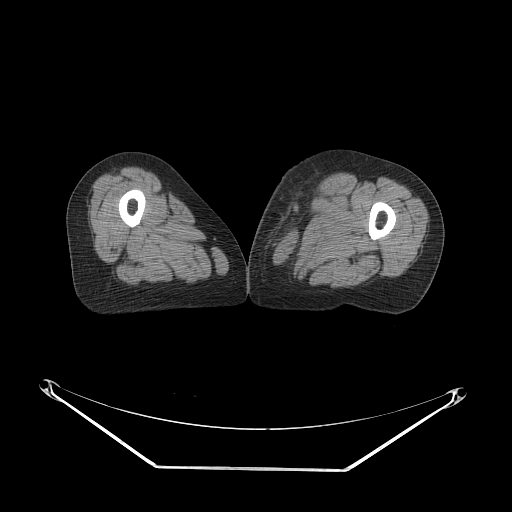
CT of an extremity soft-tissue mass (from a PET/CT study), one axial slice. Position 49 of 91 along the scan axis. Soft-tissue window (W 400 / L 40 HU). 512 × 512 image matrix, field of view 500 × 500 mm. Female patient. From the clinical record (not read from this slice): histological type: pleomorphic leiomyosarcoma; grade: high; site of the primary tumour: left thigh.
Outlined on this slice (expert contour drawn on MRI and transferred to this co-registered scan by the dataset authors):
- gross tumour volume including surrounding oedema: box from (x=263, y=183) to (x=327, y=239) px